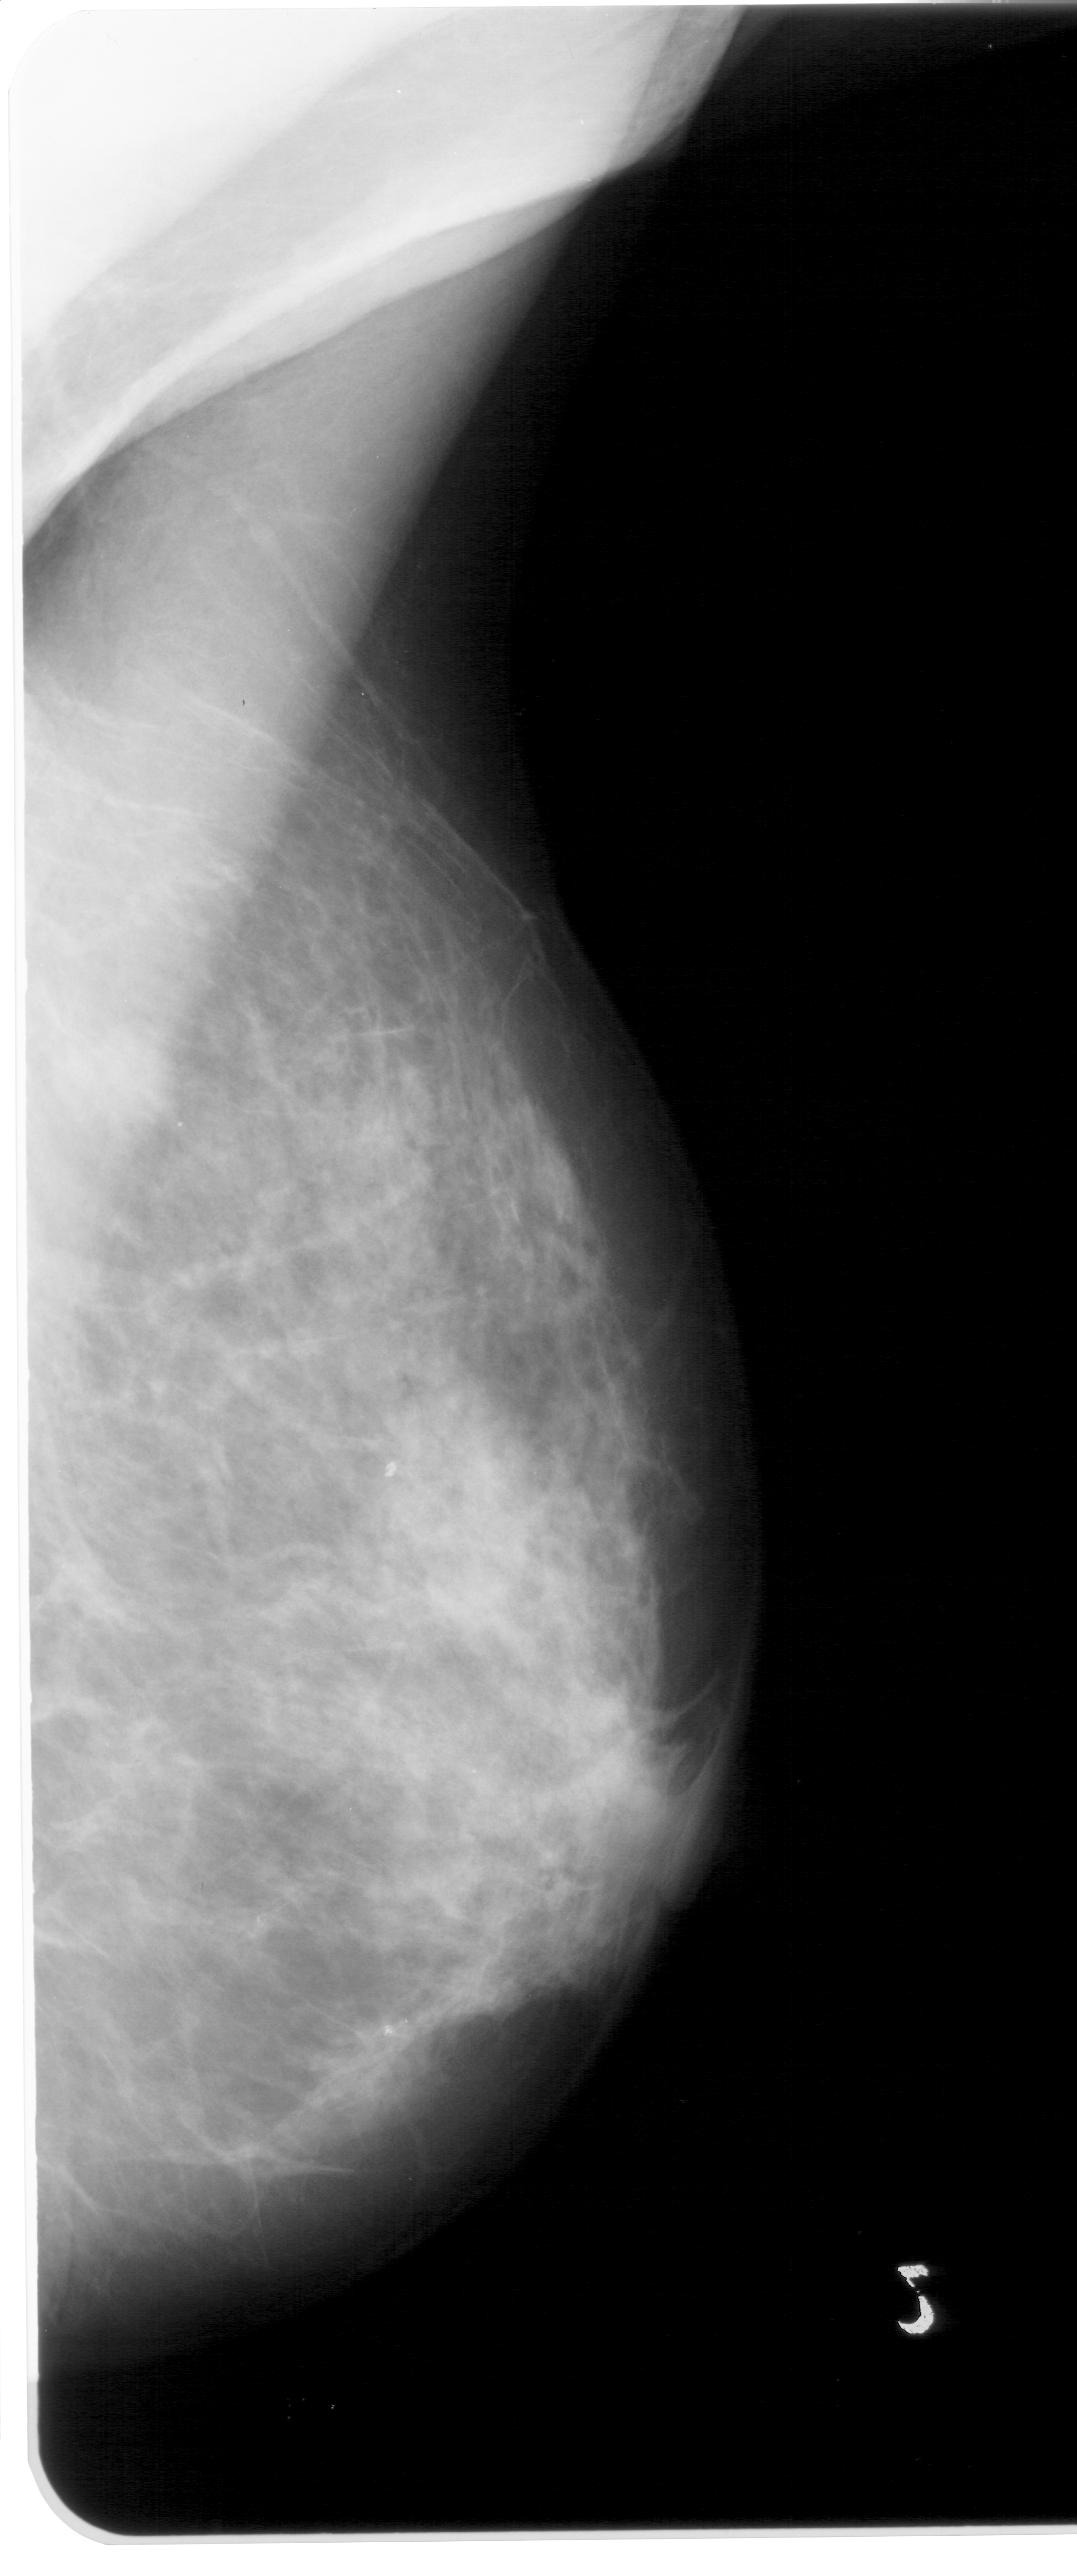
Mammogram (digitized film); right breast; MLO view; BI-RADS breast density category 4 (scale 1–4); 1077 × 2576 image matrix.
Expert-marked regions of interest on this film, with their recorded descriptors:
- mass, shape irregular, margins ill defined; BI-RADS assessment category 4; pathology (as recorded): benign: bounding box (x1, y1, x2, y2) in pixels: (57, 1018, 190, 1148)